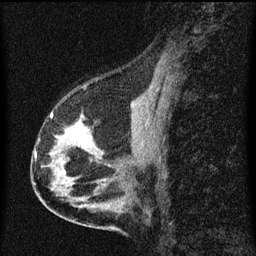
Breast MRI (dynamic contrast-enhanced), one sagittal slice. Position 31 of 60 along the scan axis. Dynamic contrast-enhanced series, image 2 of 3 at this slice position (ordered by acquisition). 1.5 T. TE 4.2 ms, TR 8 ms. 256 × 256 image matrix, field of view 180 × 180 mm. Patient: female, 56 years.
Structures marked on this image (semi-automatically segmented with operator editing):
- analysis volume of interest (the breast-tissue region the enhancement analysis was run in; not a lesion): bounding box (x1, y1, x2, y2) in pixels: (34, 114, 102, 181)
- tumour enhancement mask (voxels above the 70 % enhancement threshold inside the analysis volume of interest): (69, 122, 90, 148)